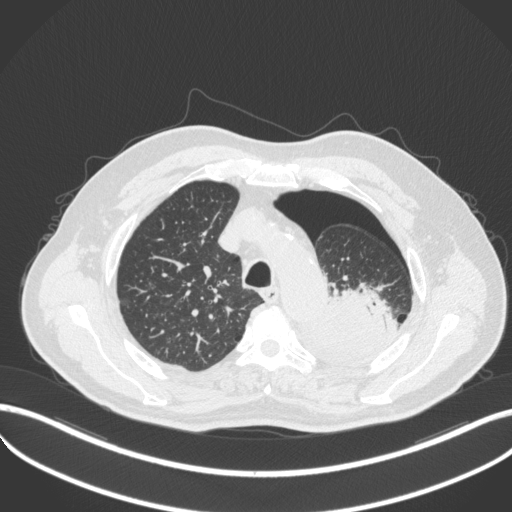
Chest CT, one axial slice. Position 391 of 466 along the scan axis. Reconstruction kernel B31f. 120 kVp. Lung window (W 1500 / L -600 HU). 1 mm slice thickness. 512 × 512 image matrix. Patient: male, 76 years. Case-level facts recorded for this patient, not image findings: clinical TNM (as recorded): T3 N0 M1b.
Outlined on this slice (rectangle marked by the reading radiologist):
- lung tumour (recorded histology: adenocarcinoma): bounding box [x1, y1, x2, y2] px = [319, 289, 387, 362]